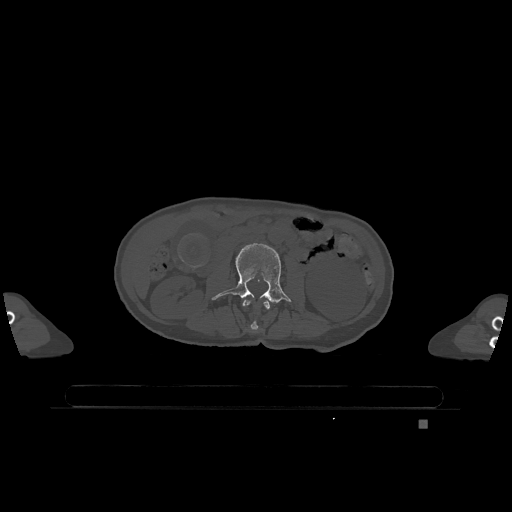
CT including the spine, one axial slice. Slice 365 of 1317 in the series (ordered by position). Bone window (W 1800 / L 400 HU). 0.5 mm slice thickness. 512 × 512 image matrix, field of view 500 × 500 mm. Patient: female, 74 years. From the clinical record (not read from this slice): primary cancer: lung; vertebrae with lytic lesions (as recorded): T1, T4, T5, T6, L4, L5.
Outlined on this slice (semi-automatically segmented with operator editing):
- L2 vertebra: box from (x=243, y=300) to (x=270, y=331) px
- L3 vertebra: (x=212, y=243)–(x=291, y=306)